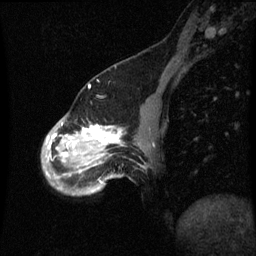
Breast MRI (dynamic contrast-enhanced), one sagittal slice; slice 16 of 60 in the series (ordered by position); dynamic contrast-enhanced series, image 2 of 3 at this slice position (ordered by acquisition); 1.5 T; TE 4.2 ms, TR 8.9 ms; 2 mm slice thickness; 256 × 256 image matrix, field of view 200 × 200 mm. Patient: female, 49 years. From the clinical record (not read from this slice): setting: breast cancer imaged before/during neoadjuvant chemotherapy; receptor status: HR-positive, HER2-negative.
Outlined on this slice (semi-automatic segmentation, software-assisted and operator-edited):
- analysis volume of interest (the breast-tissue region the enhancement analysis was run in; not a lesion): bounding box [x1, y1, x2, y2] px = [42, 112, 145, 197]
- tumour enhancement mask (voxels above the 70 % enhancement threshold inside the analysis volume of interest): [46, 126, 121, 157]